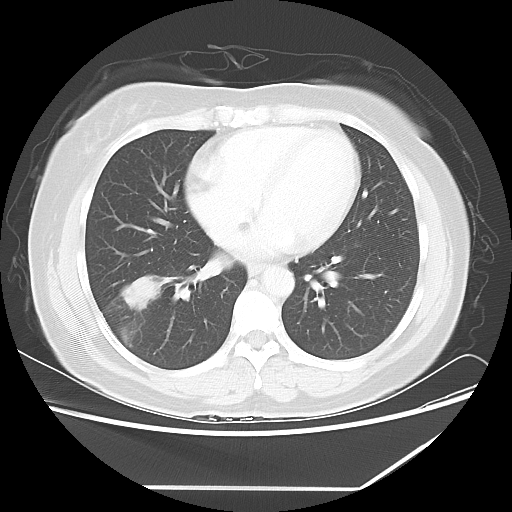
Chest CT, one axial slice; slice 26 of 60 in the series (ordered by position); 100 kVp; lung window (W 1500 / L -600 HU); 5 mm slice thickness; 512 × 512 image matrix, field of view 374 × 374 mm. Female patient, age 42 years. Case-level facts recorded for this patient, not image findings: clinical TNM (as recorded): T2 N1 M0.
Outlined on this slice (bounding box drawn by a radiologist):
- lung tumour (recorded histology: adenocarcinoma): bounding box (x1, y1, x2, y2) in pixels: (113, 267, 170, 313)